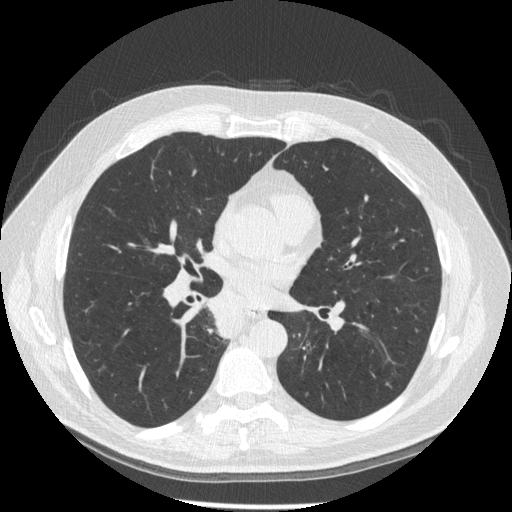
Low-dose screening chest CT, one axial slice. Slice 94 of 181 in the series (ordered by position). Lung window (W 1500 / L -600 HU). 512 × 512 image matrix, field of view 370 × 370 mm.
Structures marked on this image (expert manual segmentation):
- lesion 1 (tumor, lower lobe of right lung): bounding box (x1, y1, x2, y2) in pixels: (207, 299, 243, 338)